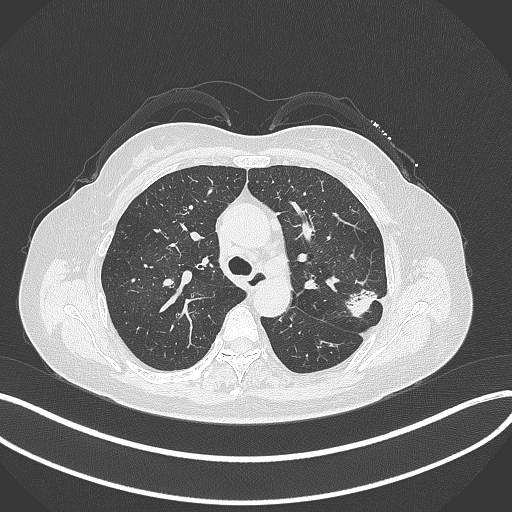
Chest CT, one axial slice. Slice 221 of 319 in the series (ordered by position). Reconstruction kernel B70f. 120 kVp. Lung window (W 1500 / L -600 HU). 1 mm slice thickness. 512 × 512 image matrix, field of view 400 × 400 mm. Female patient, age 60 years. From the clinical record (not read from this slice): clinical TNM (as recorded): T1c N0 M0.
Structures marked on this image (bounding box drawn by a radiologist):
- lung tumour (recorded histology: adenocarcinoma): bounding box [x1, y1, x2, y2] px = [340, 287, 378, 318]